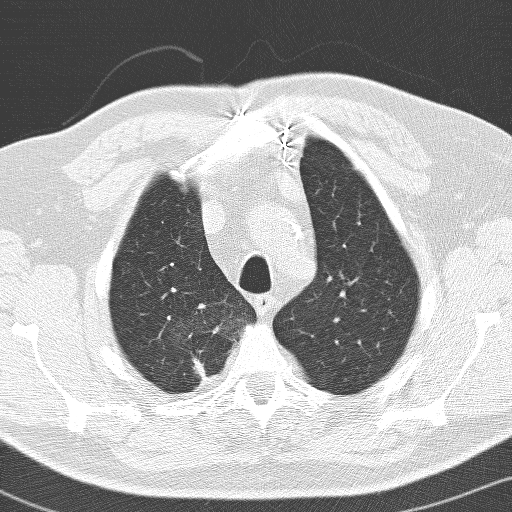
Low-dose screening chest CT, one axial slice. Slice 119 of 141 in the series (ordered by position). 120 kVp. Lung window (W 1500 / L -600 HU). 3.2 mm slice thickness. 512 × 512 image matrix, field of view 326 × 326 mm.
Structures marked on this image (expert manual segmentation):
- lesion 1 (tumor, upper lobe of right lung): bounding box <194,351,206,378> (left, top, right, bottom; pixels)